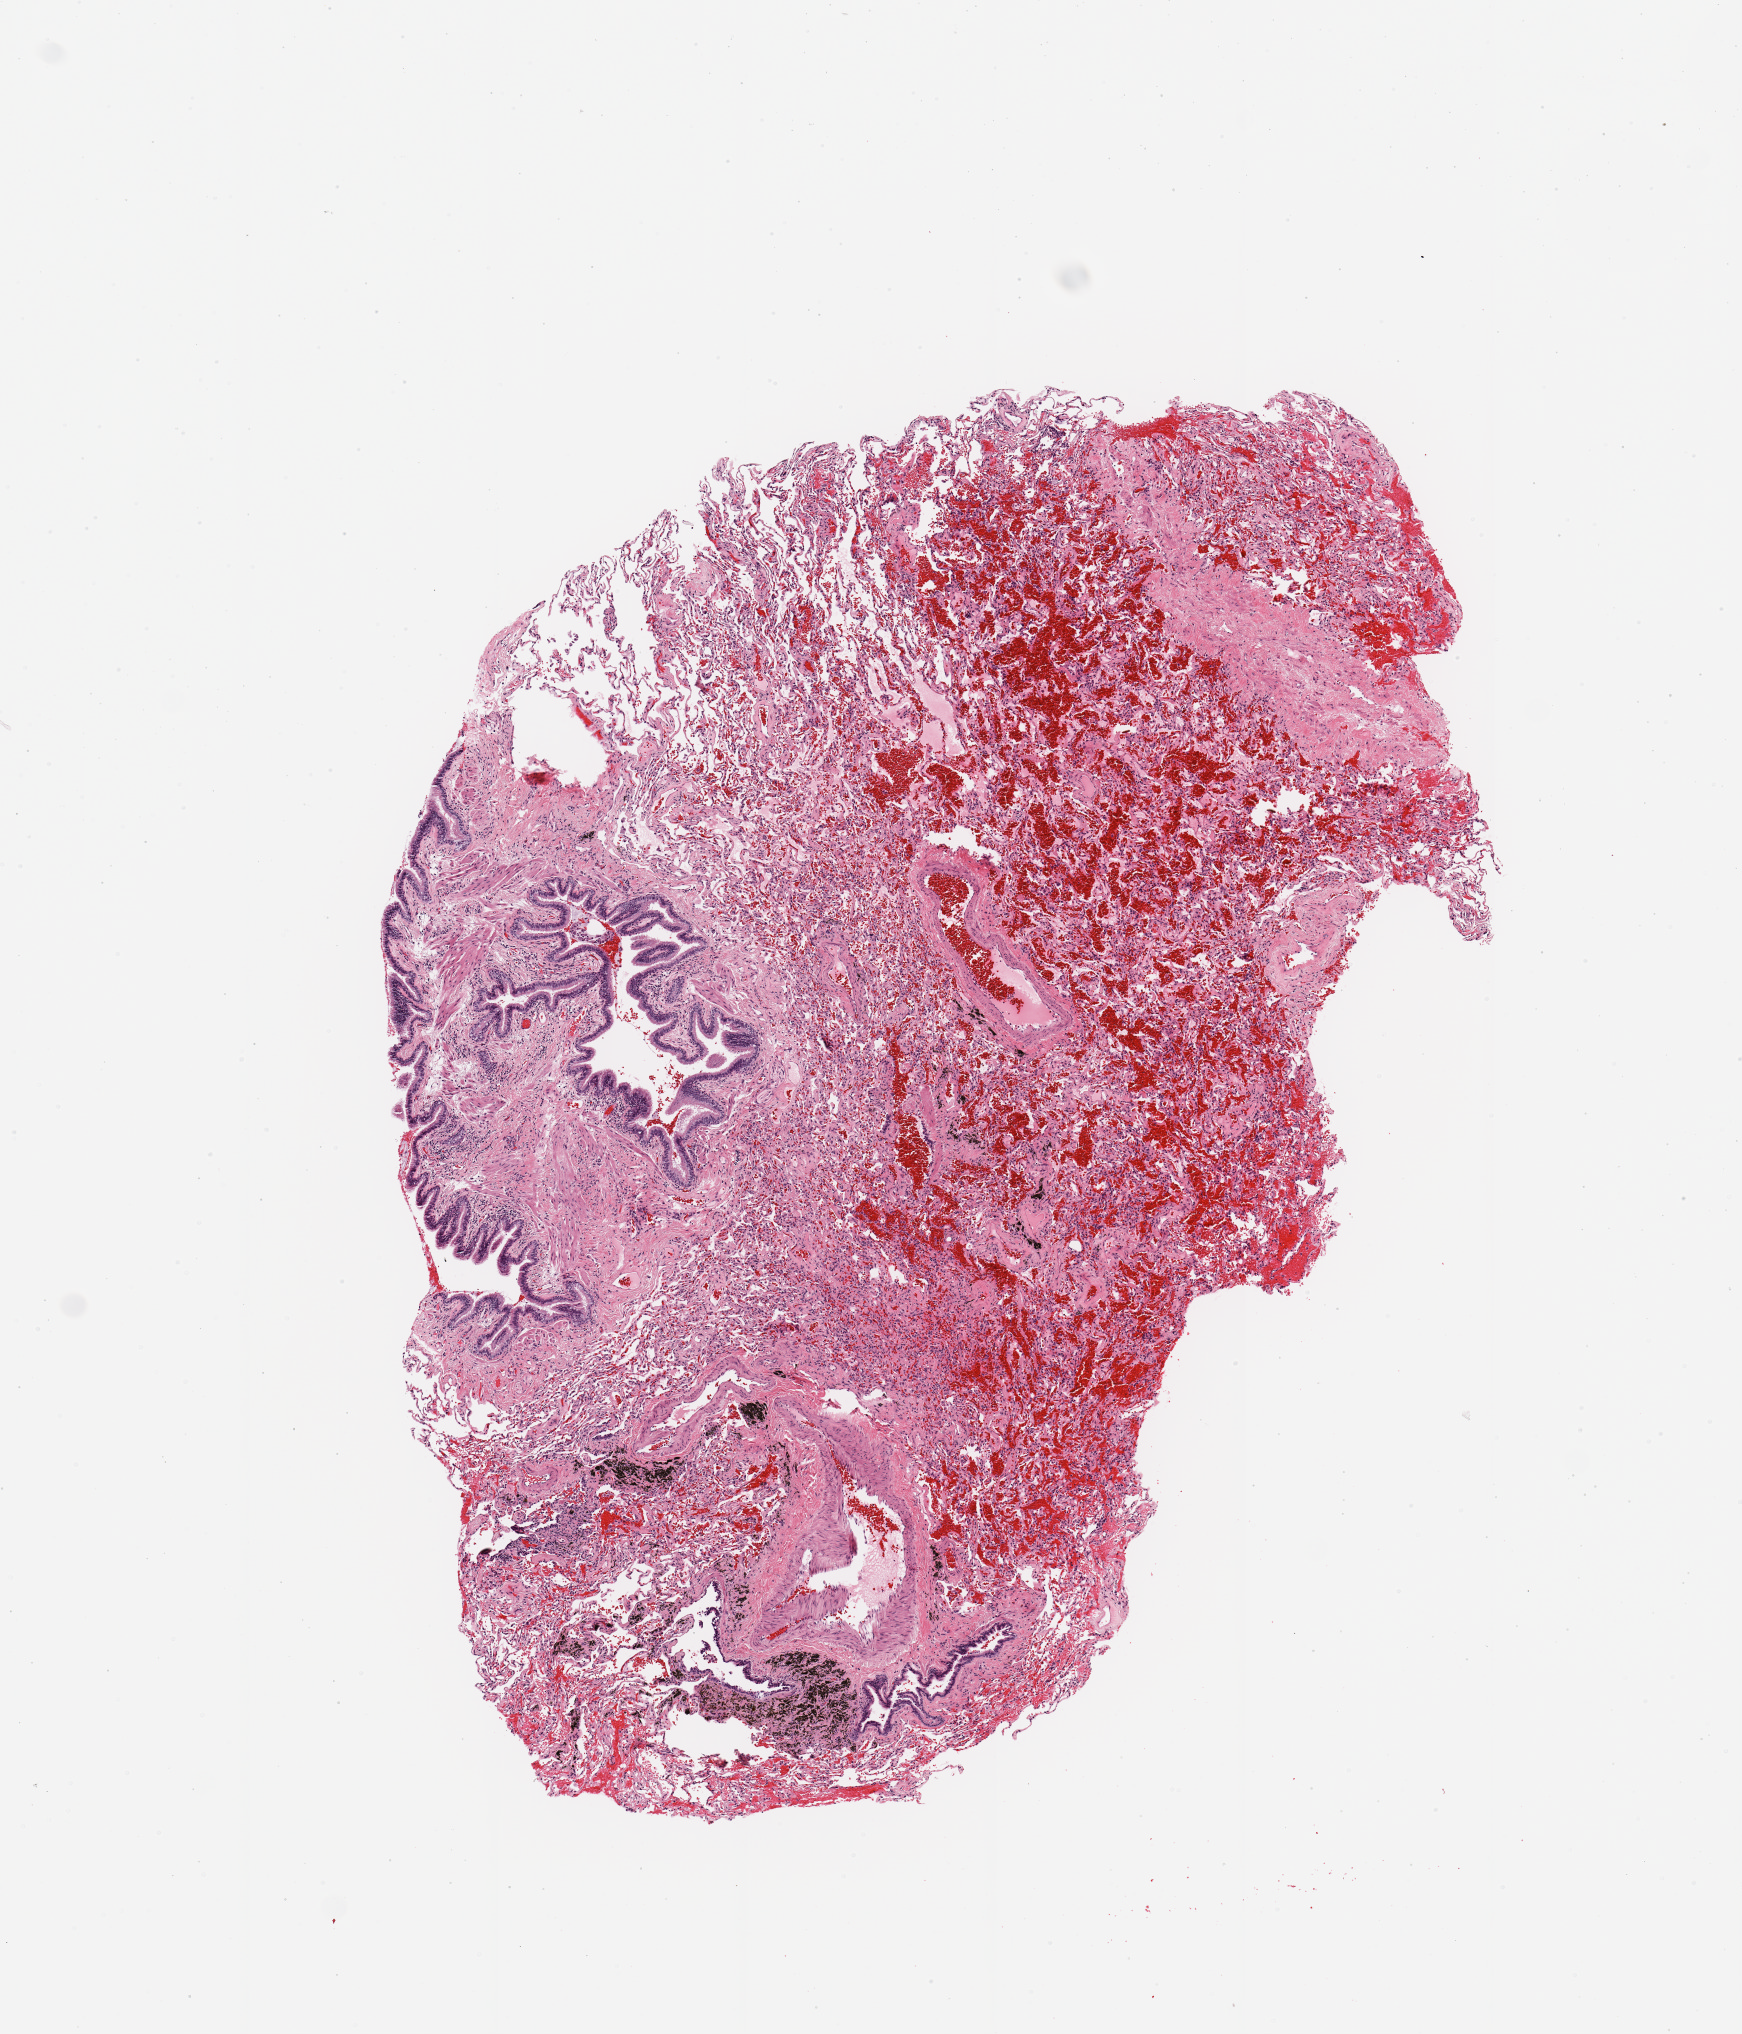
Hematoxylin and eosin (H&E) stained whole-slide image — whole scanned area (about 6.9 x 8.0 mm) shown as a low-resolution overview; normal (non-tumour) tissue sample, sampled site: lung. 69-year-old male patient.
This section: normal (non-tumour) tissue from the same patient. Patient diagnosis: Adenocarcinoma, NOS.